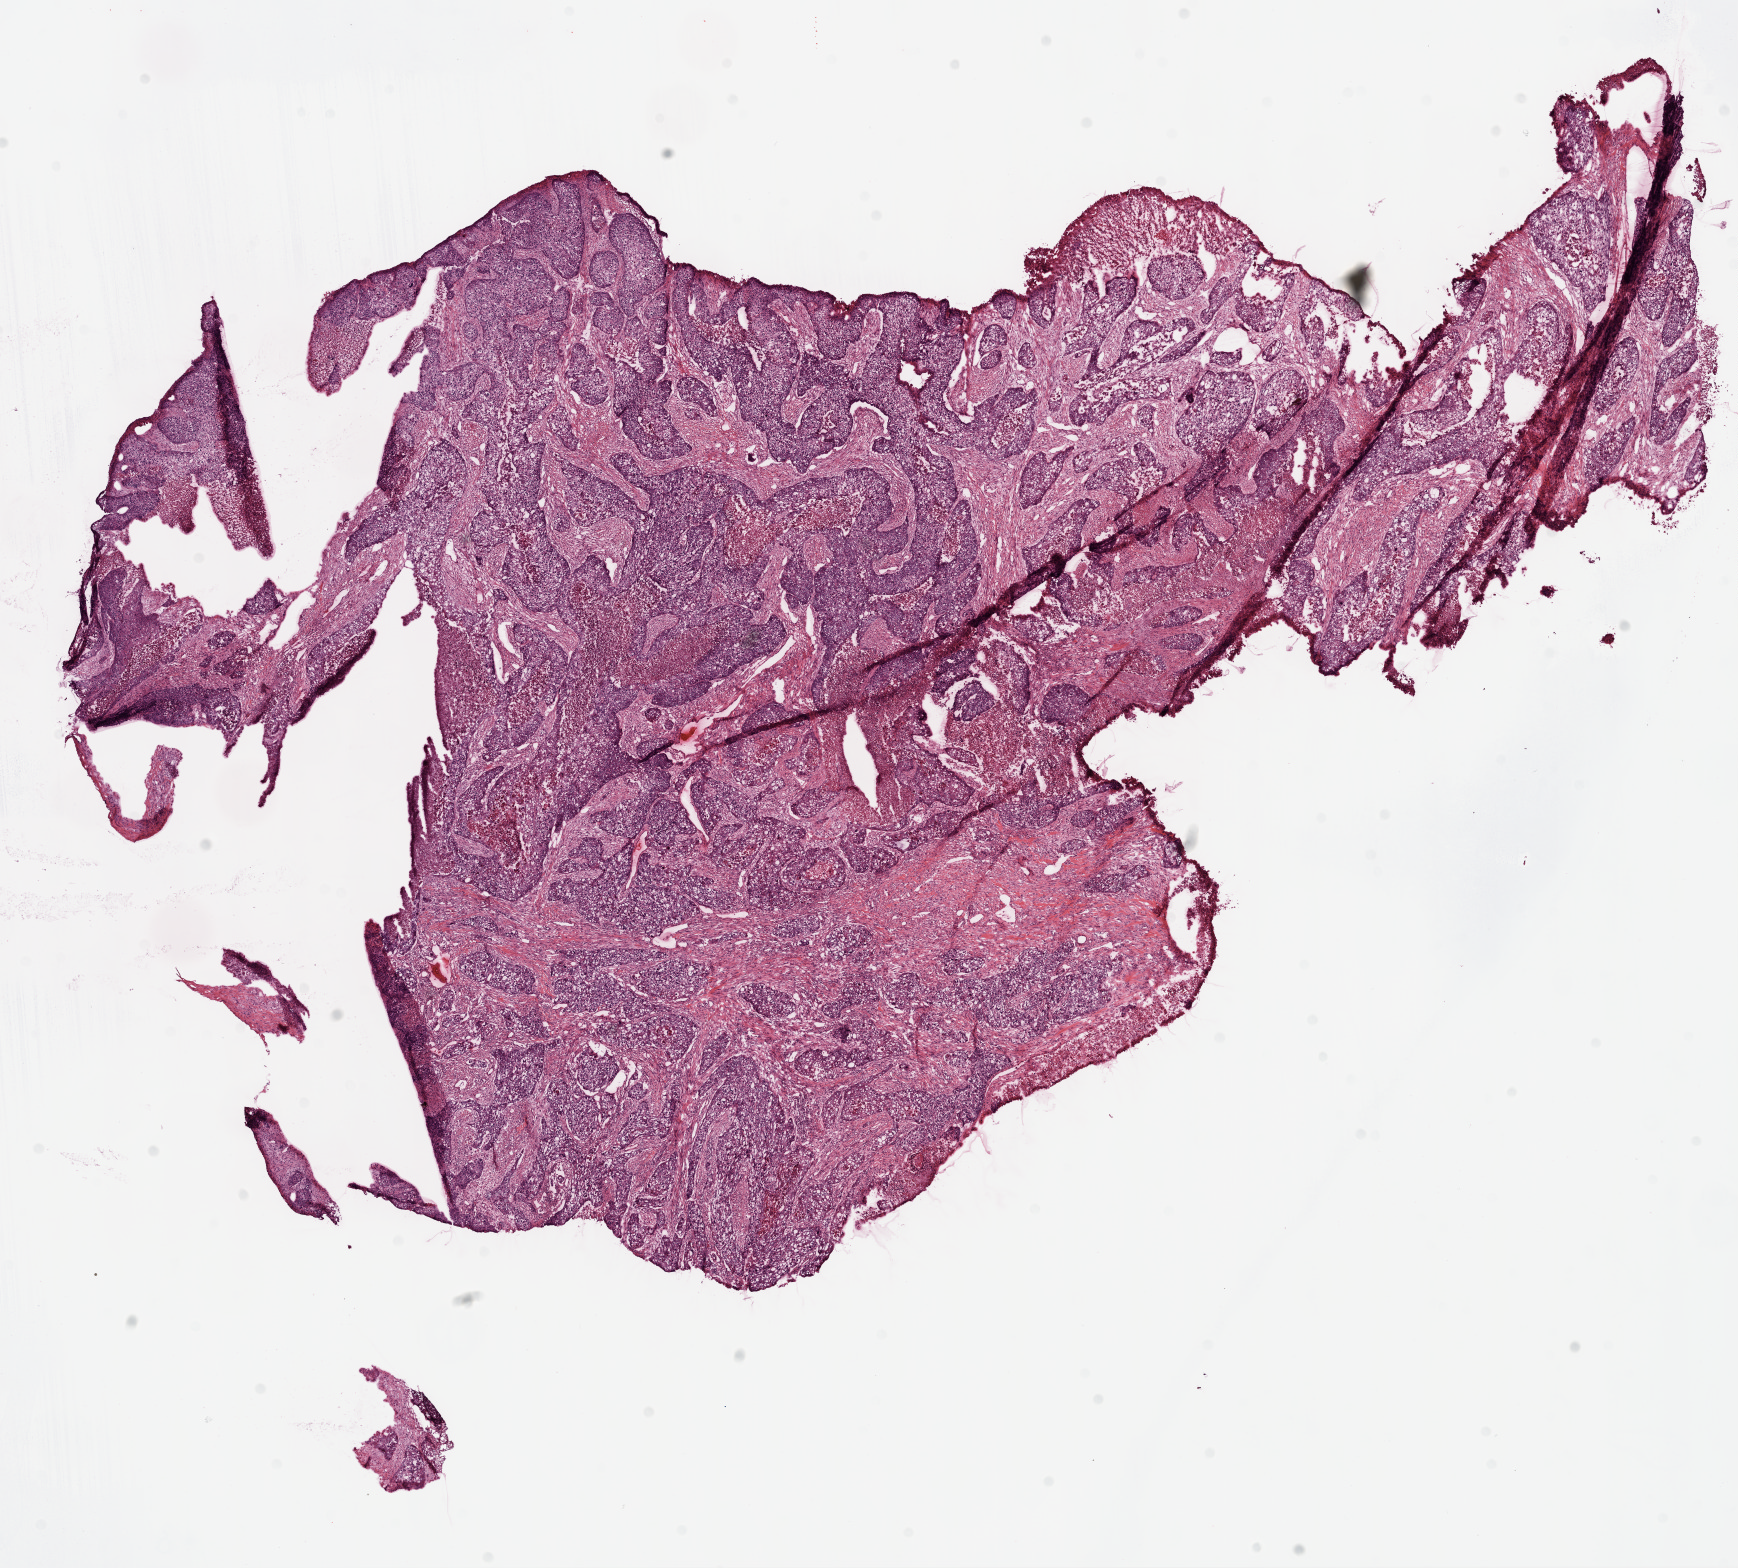
Whole-slide histology image, H&E, whole scanned area (about 14.0 x 12.6 mm, from a 20x scan) shown as a low-resolution overview. Frozen section from the top of the tissue portion. Primary tumour sample from the lung. Male patient; age at initial diagnosis 69 years. Composition of this section per pathologist review: tumour nuclei 85%, necrosis 4%.
Laterality: left. Diagnosis: Squamous cell carcinoma, NOS (lower lobe, lung). AJCC pathologic stage: IIB.